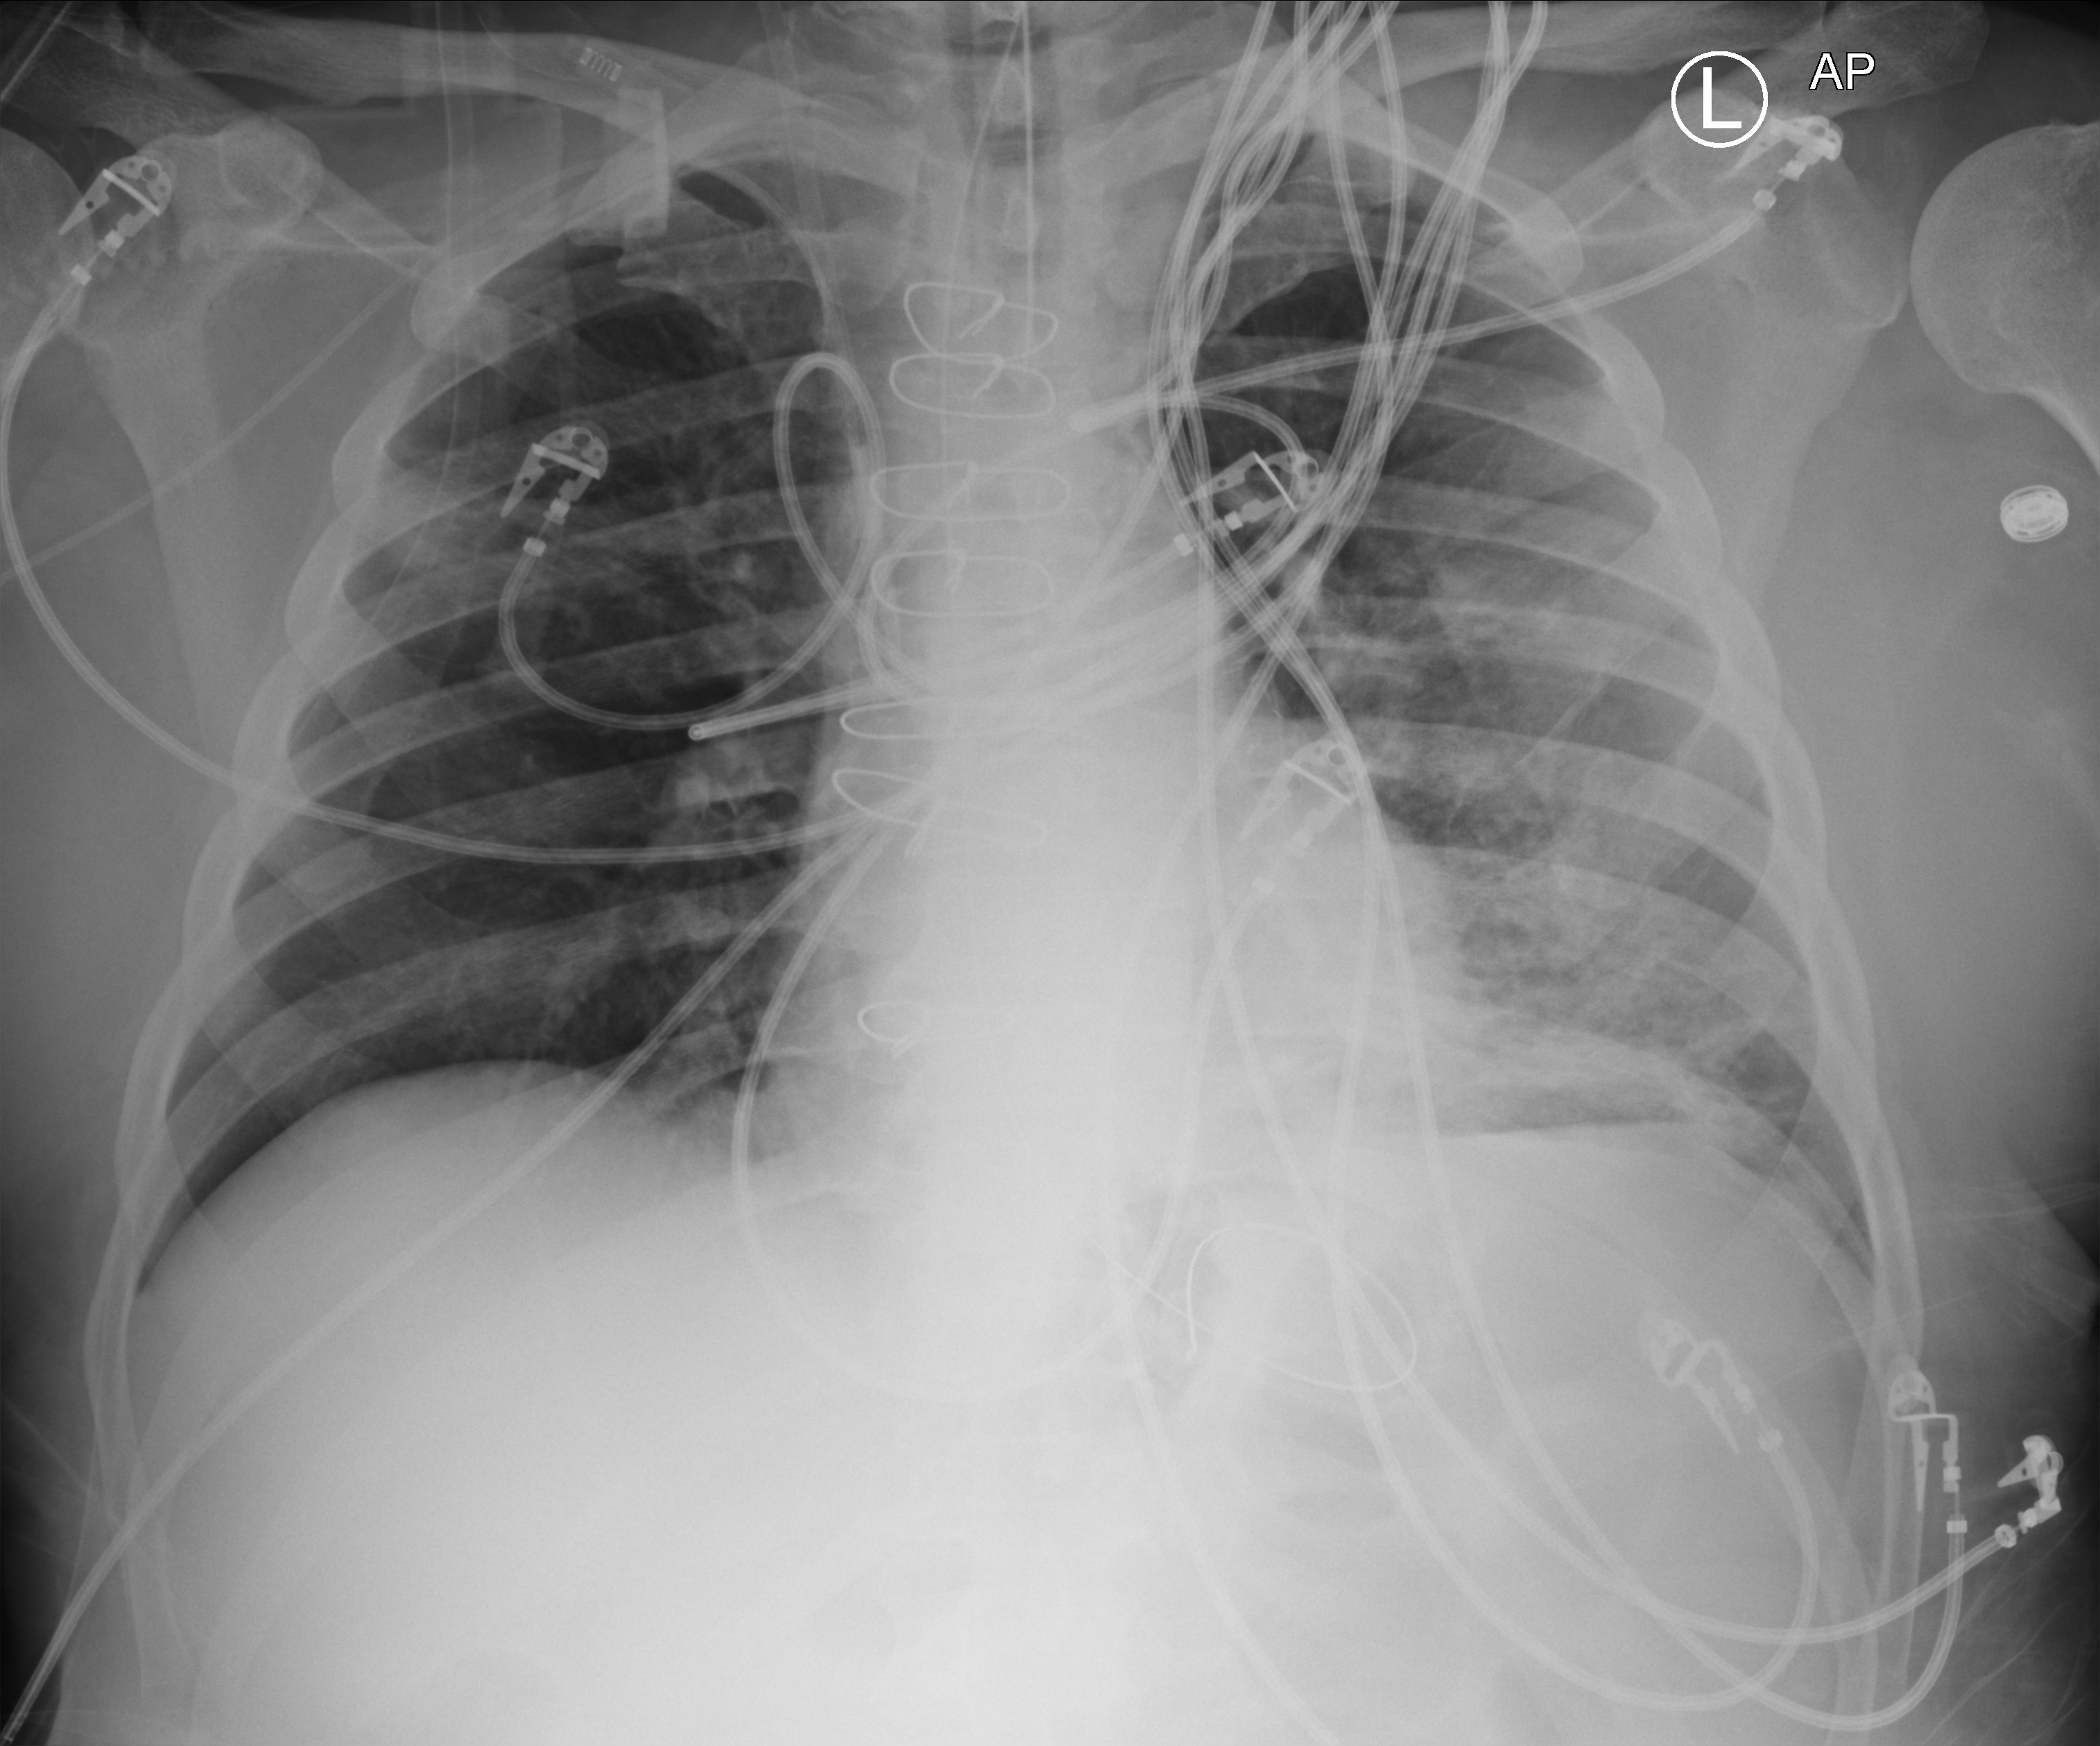
Portable chest radiograph, anteroposterior (AP) projection. Patient hospitalised with COVID-19; male, aged 60–74 years.
Admission-level facts for this patient (not findings on this image; timing relative to this image not recorded): chronic kidney disease (admission record): no.